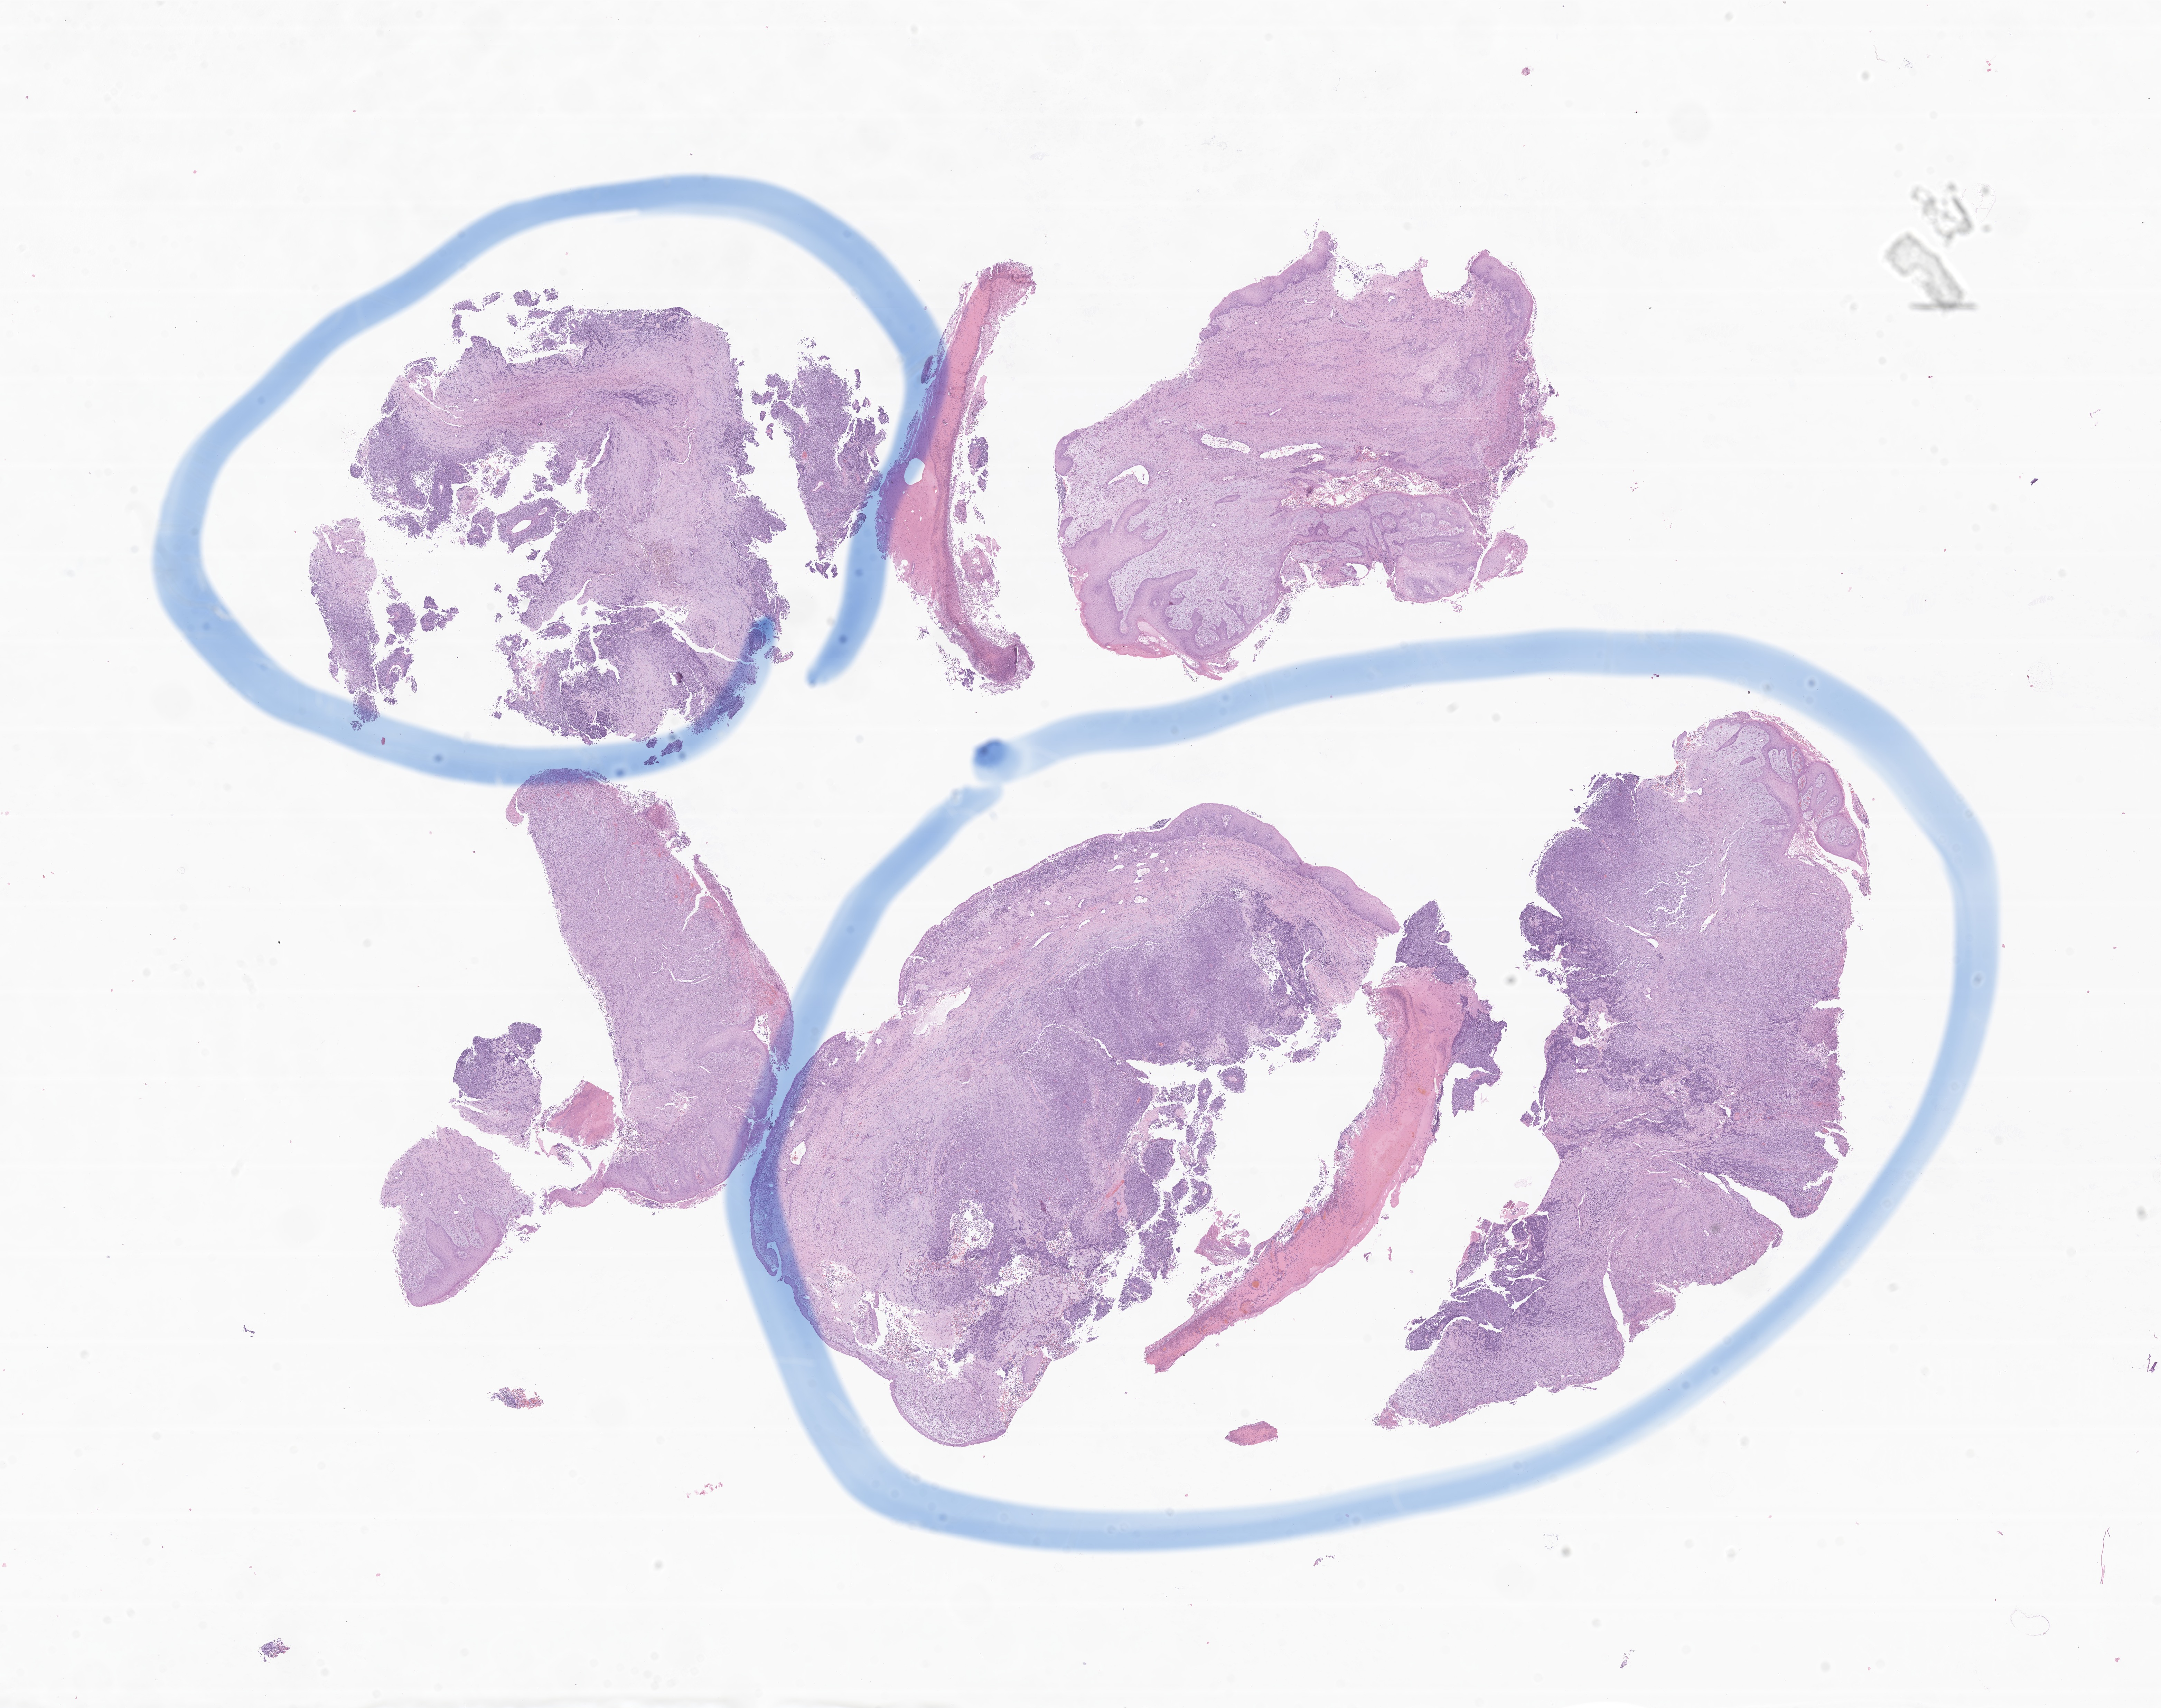
Whole-slide image, haematoxylin and eosin stain of tumor tissue from the nasal cavity — shown as a low-resolution overview of the whole scanned area (about 26.4 x 20.8 mm); formalin-fixed paraffin-embedded section. Male patient, age 239 days.
• diagnosis (ICD-O-3 morphology term): Rhabdomyosarcoma, NOS